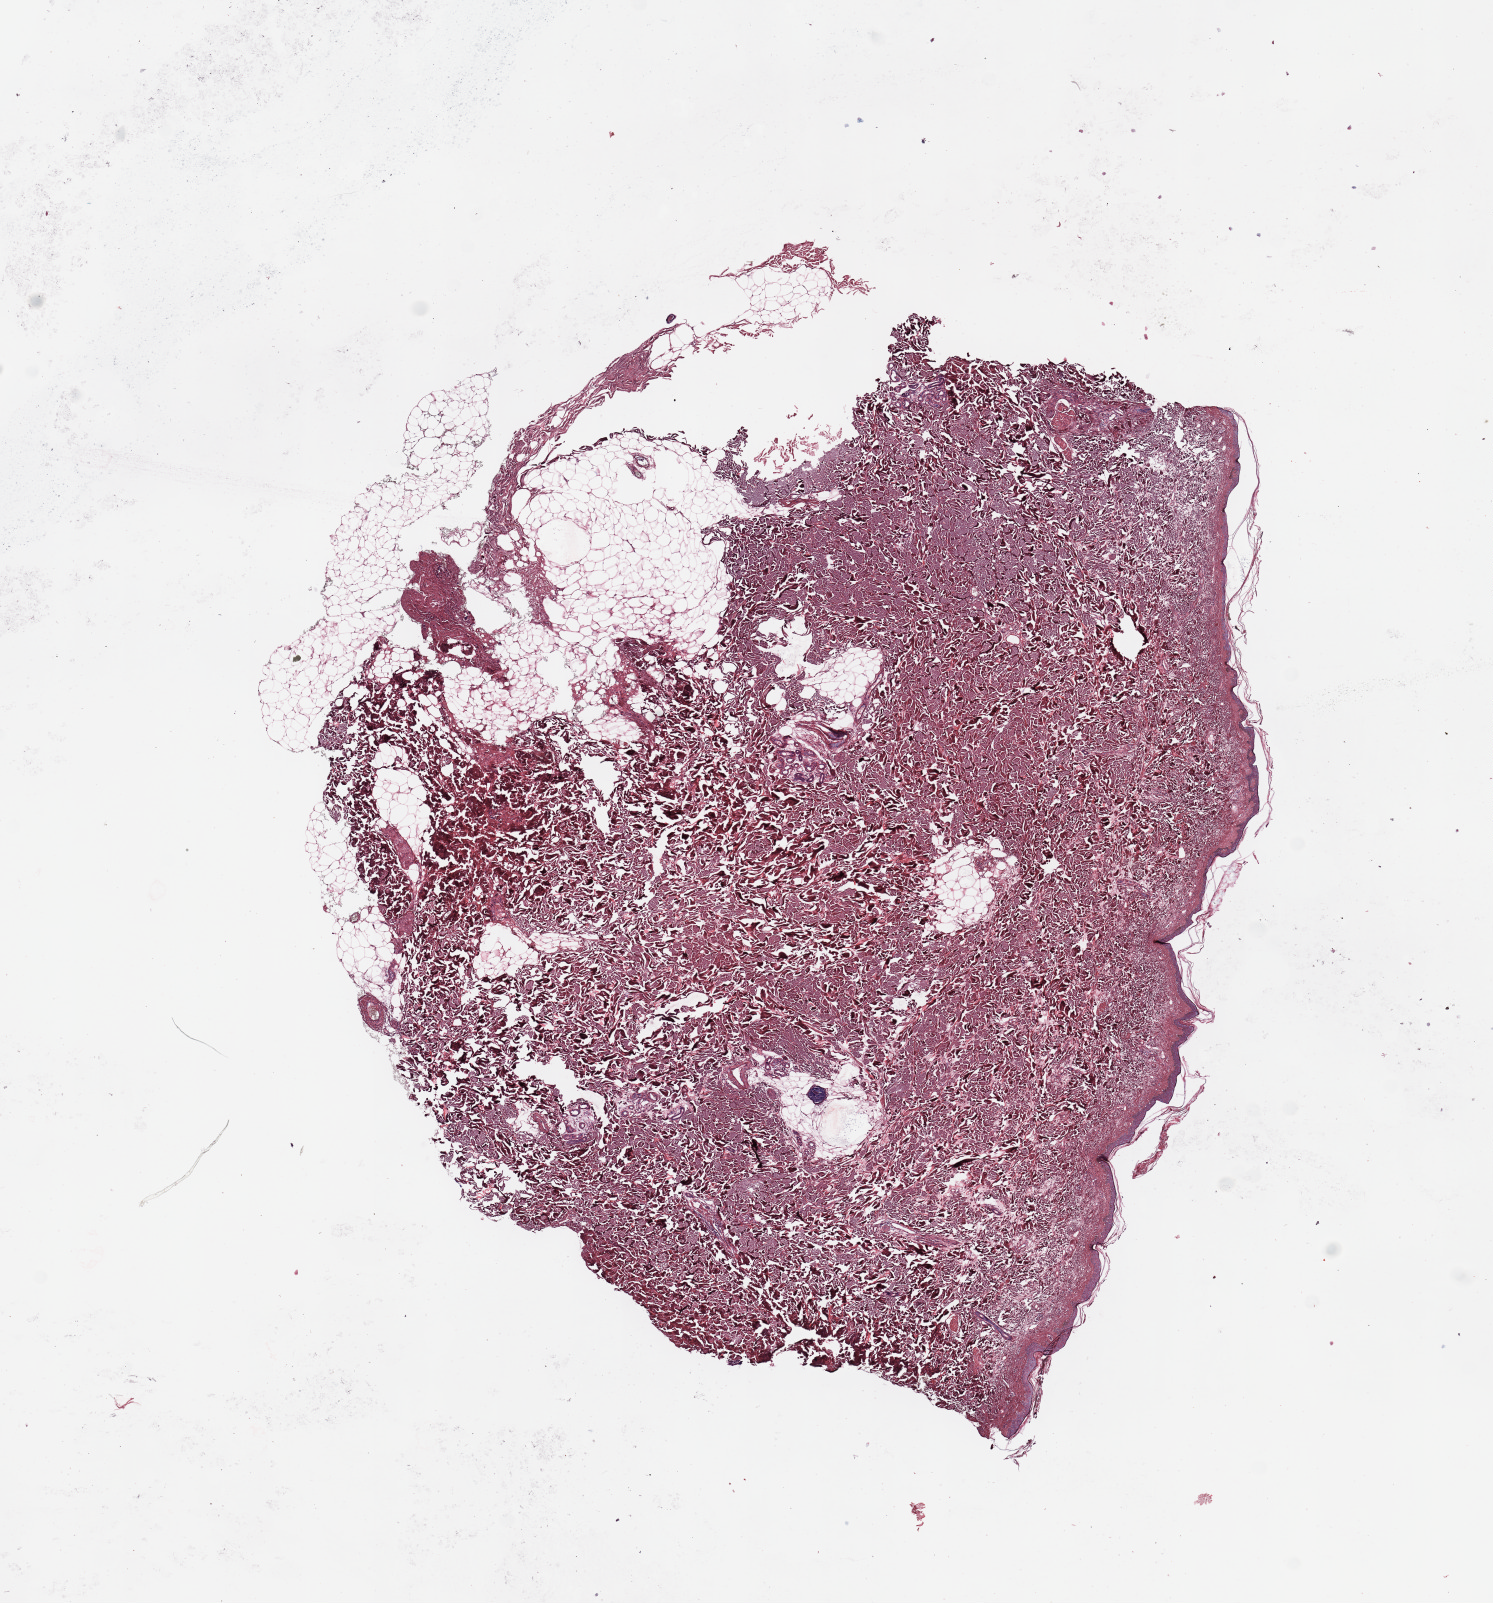
H&E-stained whole-slide image — low-resolution overview of the scanned area, about 11.8 x 12.7 mm (acquisition: 20x scan). Normal (non-tumour) tissue sample, sampled site: trunk. 83-year-old male patient.
This section: normal (non-tumour) tissue from the same patient. Patient diagnosis: Malignant melanoma, NOS.